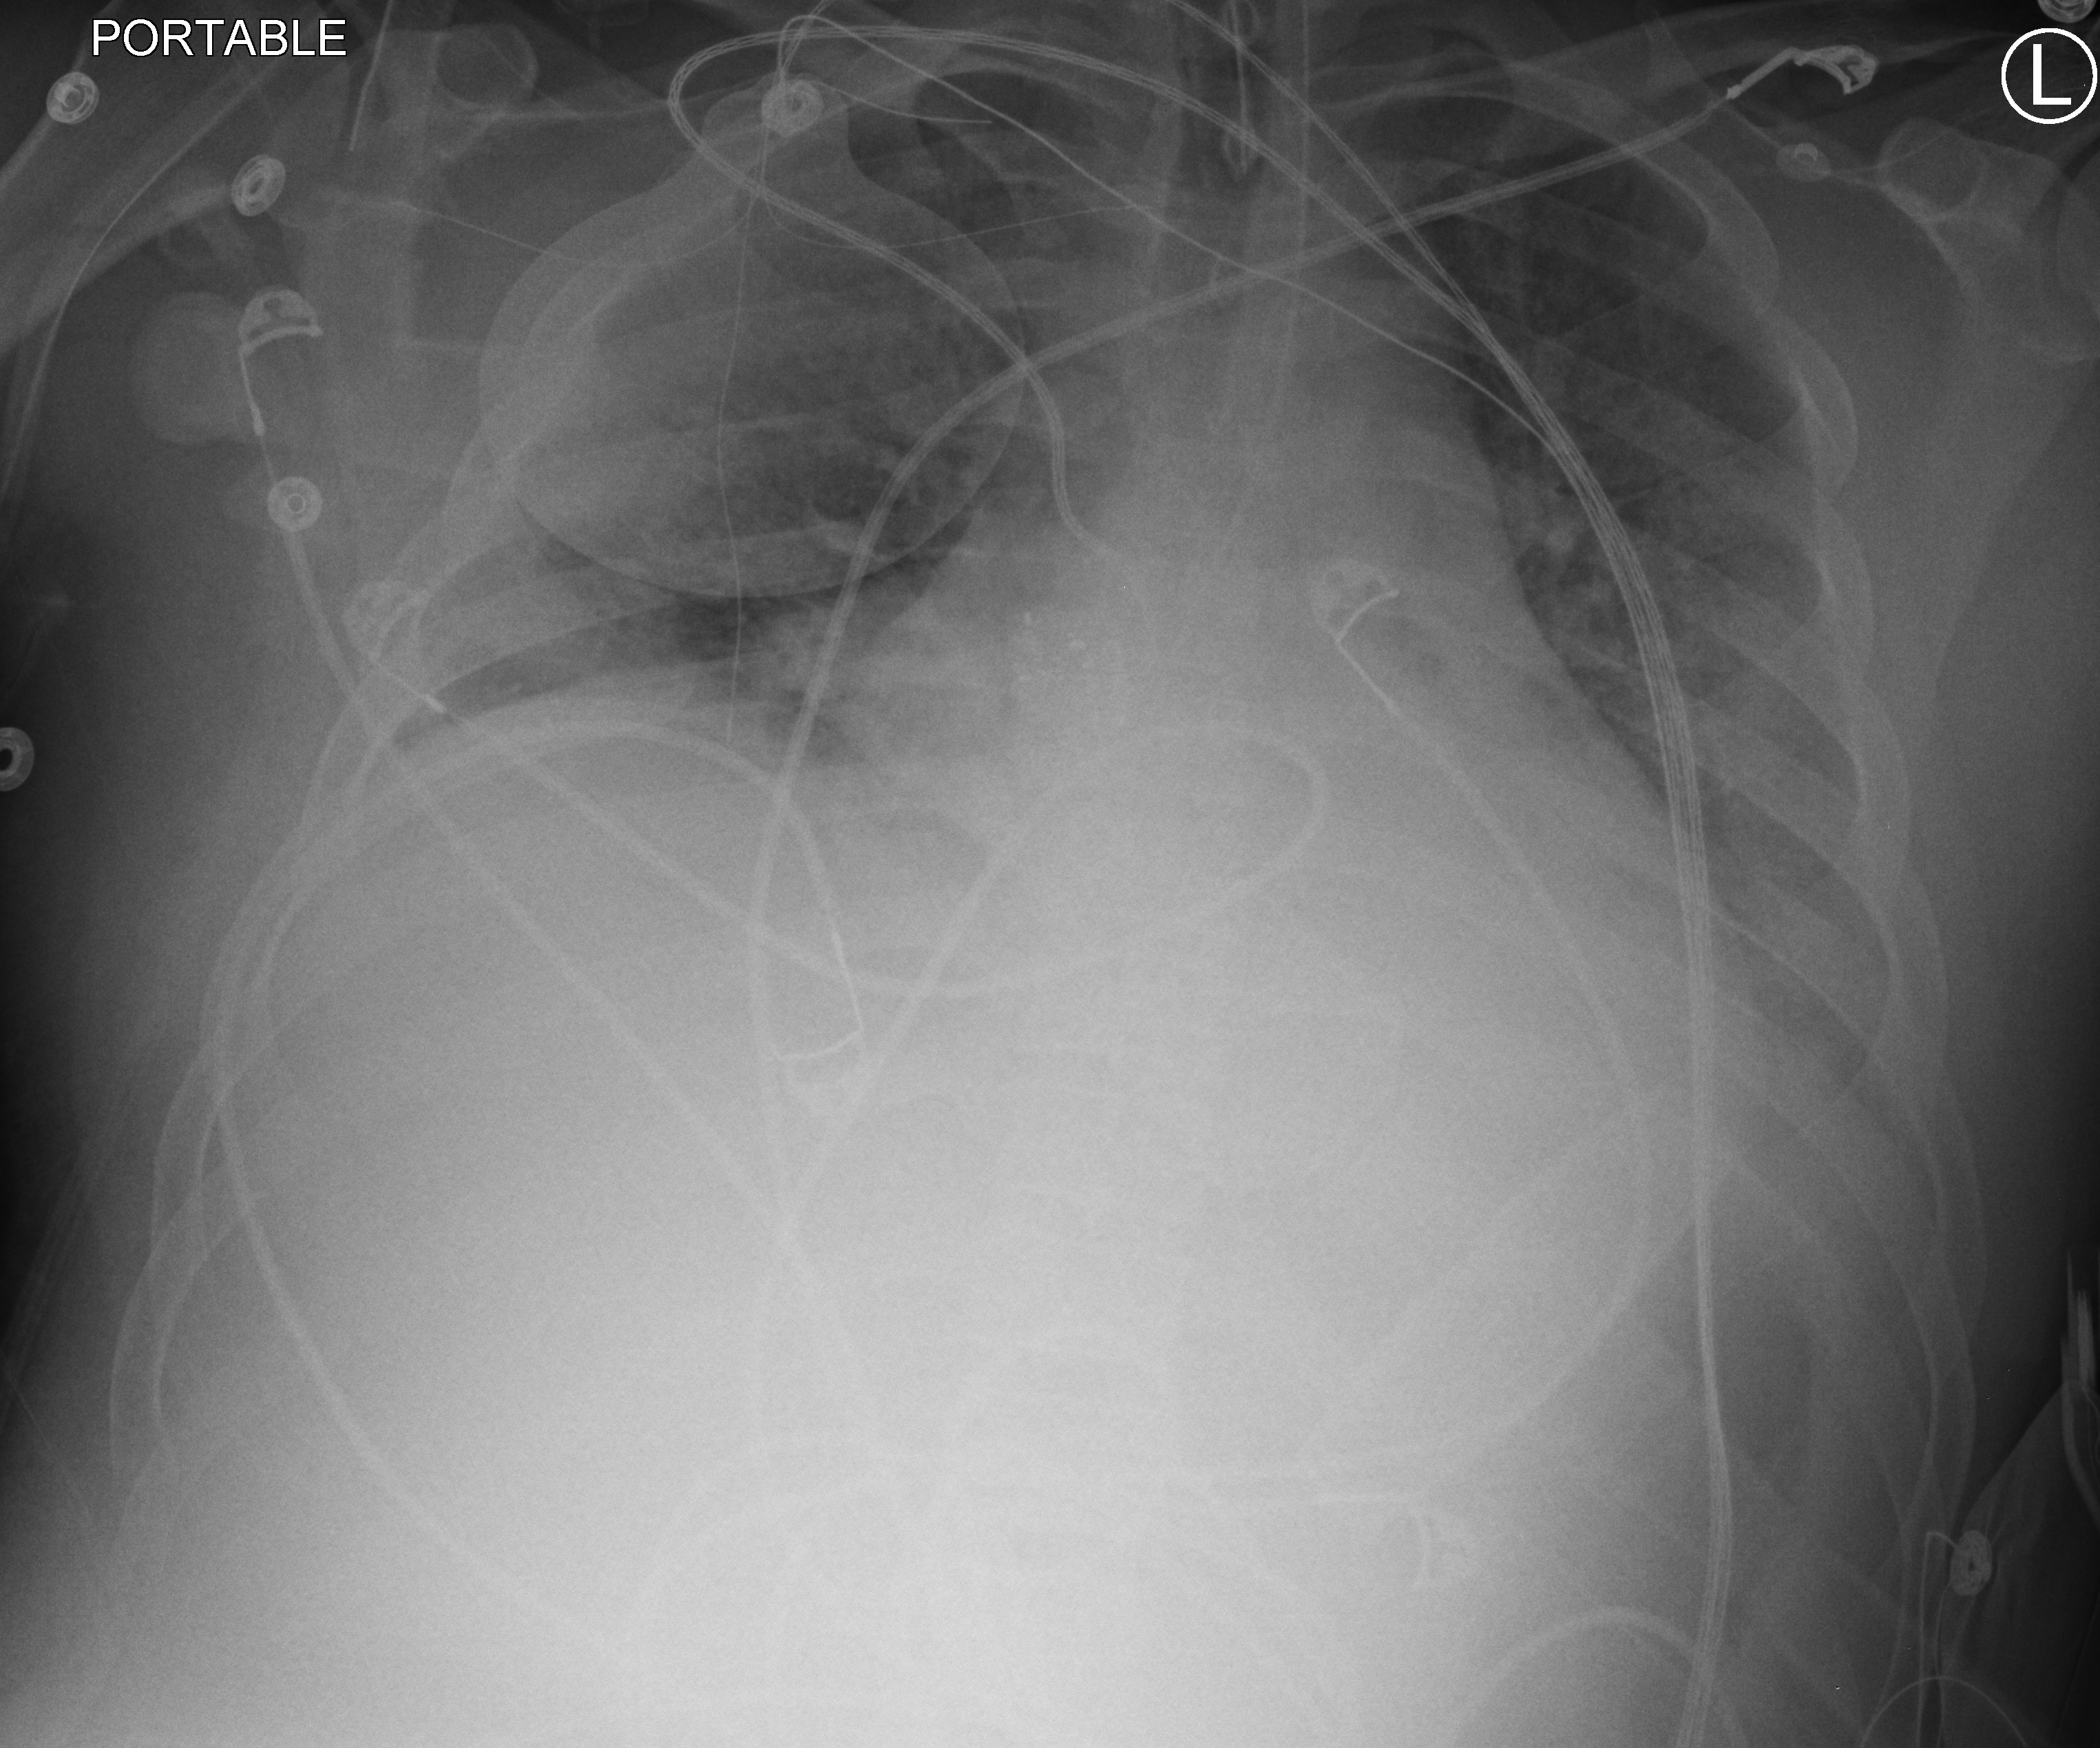
Portable chest radiograph; anteroposterior (AP) projection. Male patient hospitalised with COVID-19, age 18–59 years.
Admission-level facts for this patient (not findings on this image; timing relative to this image not recorded): admitted to intensive care during this hospital stay: yes.